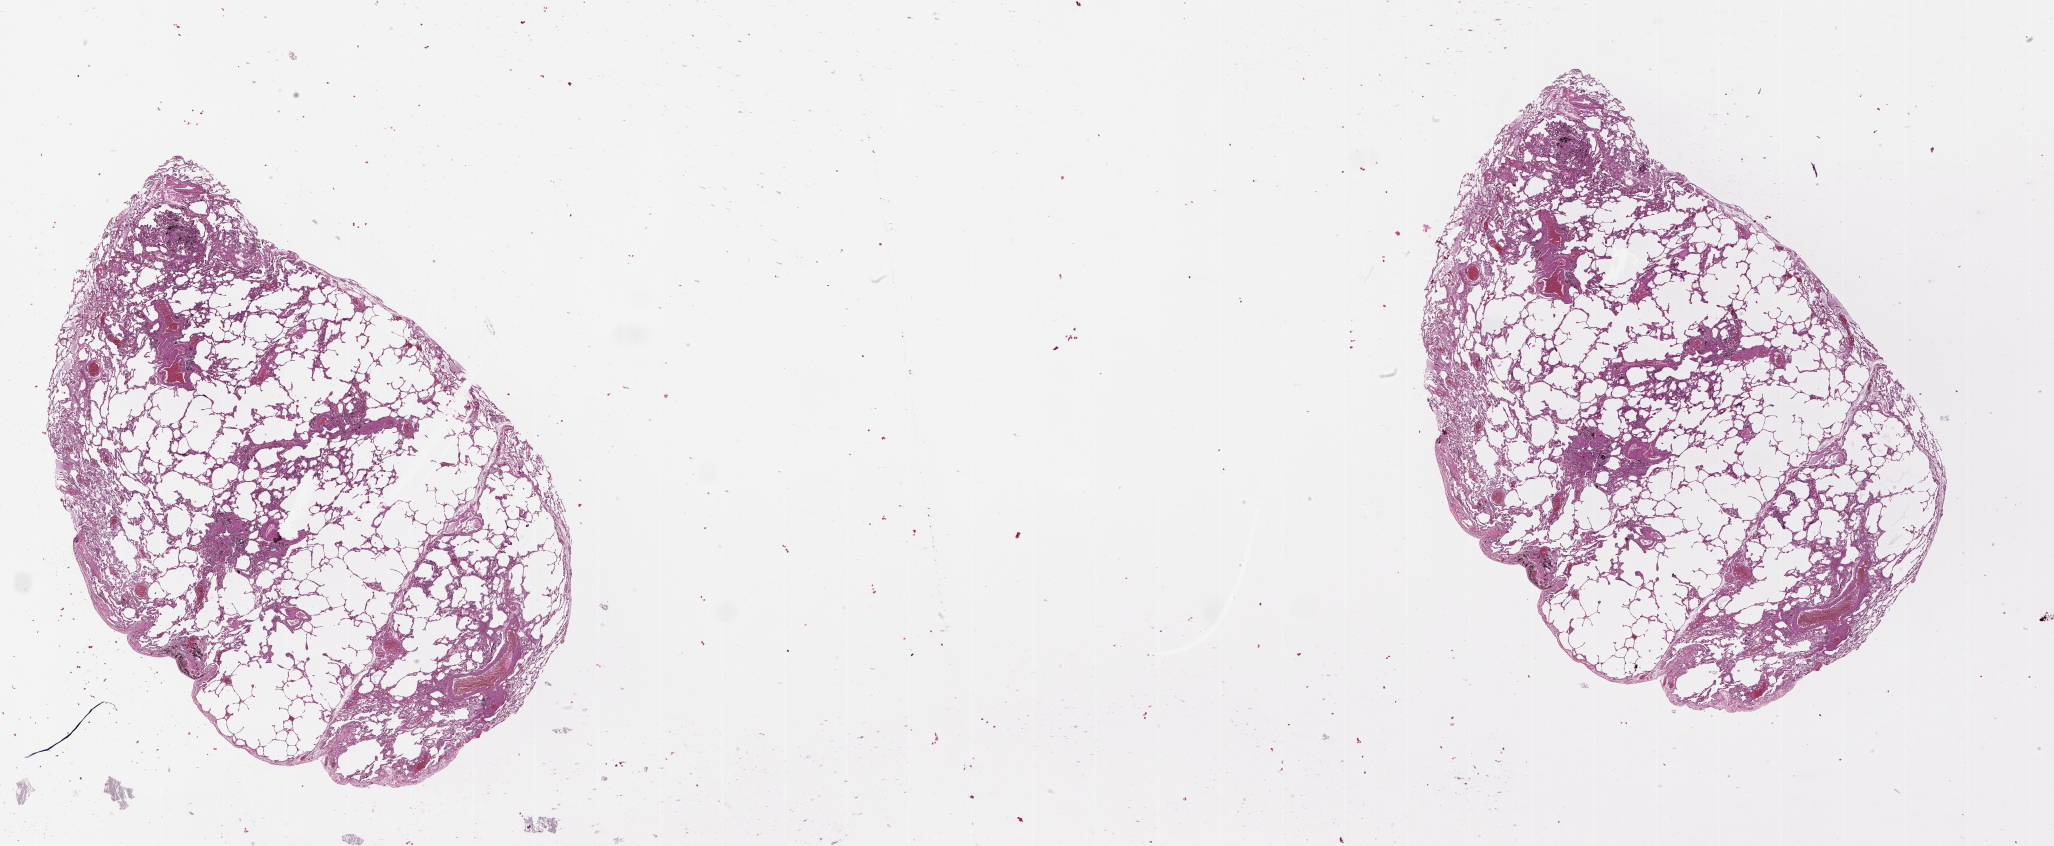
H&E-stained whole-slide image — a low-resolution overview of the entire scanned area, about 33.1 x 13.6 mm (acquisition: 20x scan), lung, normal (non-tumour) tissue. Patient: male, age 65 years.
- this section: normal (non-tumour) tissue from the same patient
- patient diagnosis (cohort enrolment): squamous cell carcinoma (lung)